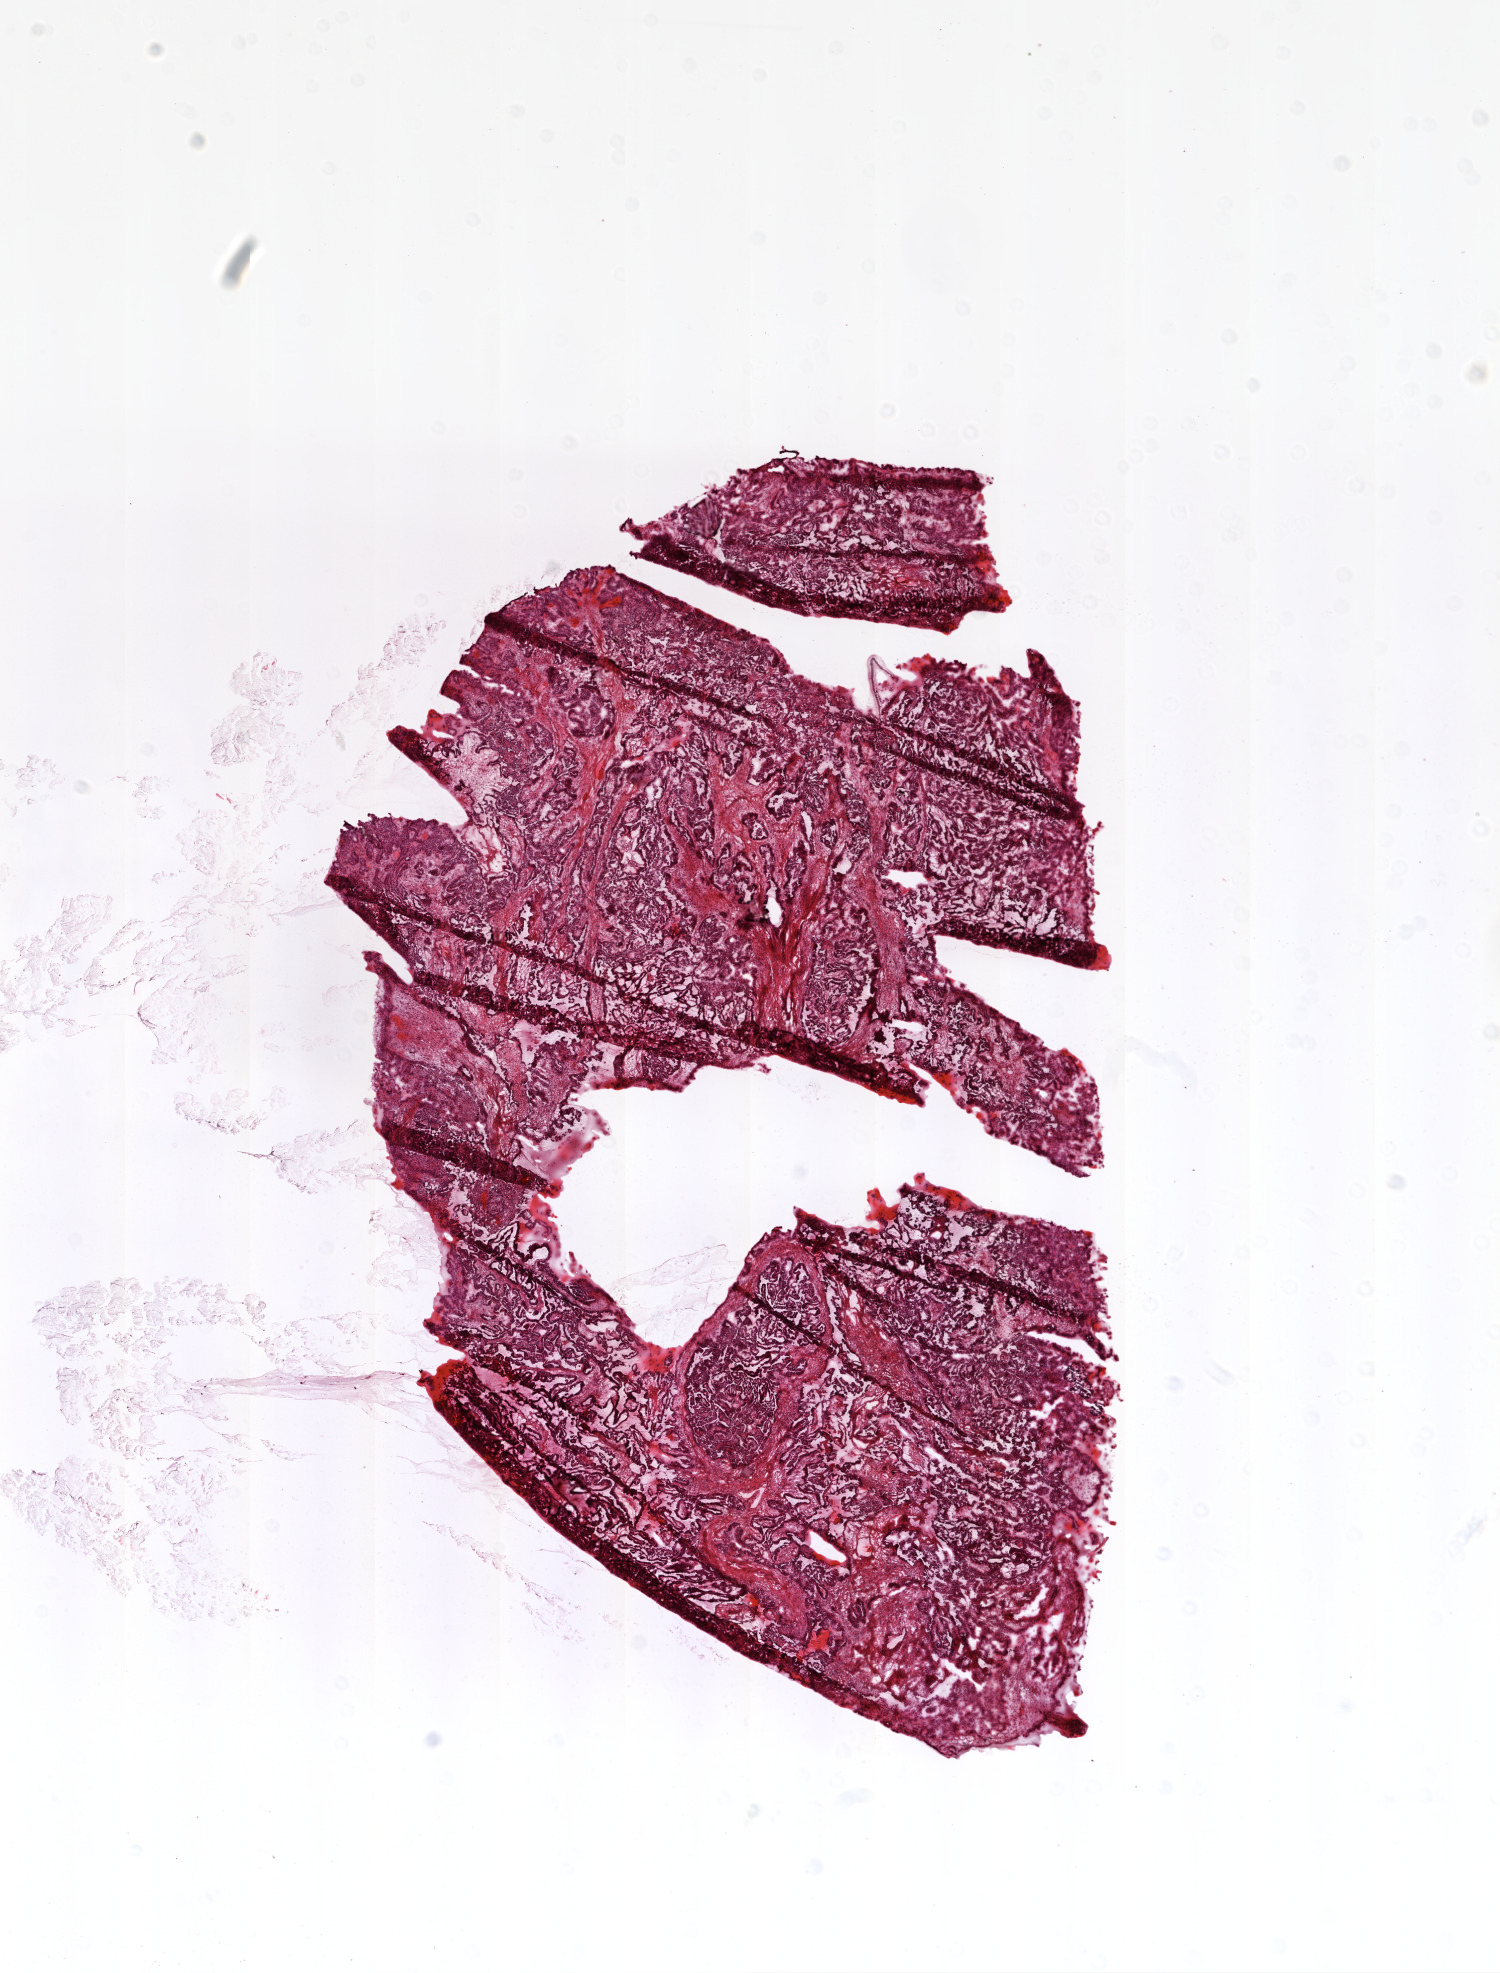
Digitized H&E-stained tissue section (whole slide) — a low-resolution overview of the entire scanned area, about 12.0 x 15.8 mm (acquisition: 20x scan), frozen section, primary tumour sample from the ovary. Female, age 64 years at initial diagnosis. Histologic grade: G3 (poorly differentiated). Slide review estimates, as recorded: tumour cells 80%, tumour nuclei 80%, normal cells 0%, stromal cells 20%, necrosis 0%. Inflammatory infiltration, as recorded: lymphocyte infiltration 0%, monocyte infiltration 0%, neutrophil infiltration 0%.
• FIGO stage: IIIC
• histologic diagnosis: Serous cystadenocarcinoma, NOS